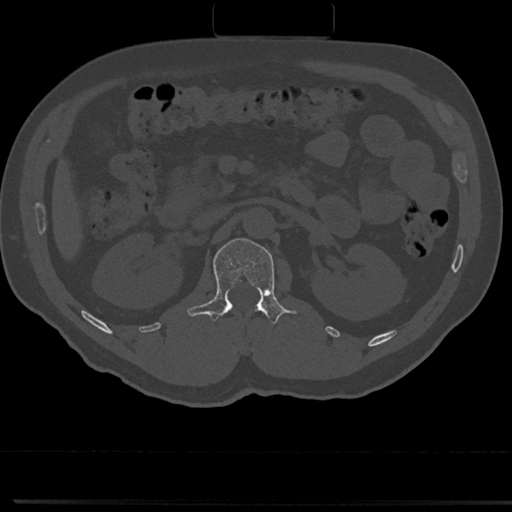
CT including the spine, one axial slice; slice 87 of 817 in the series (ordered by position); reconstruction kernel Br40s/3; 120 kVp; bone window (W 1800 / L 400 HU); 0.5 mm slice thickness; 512 × 512 image matrix. Male patient, age 61 years. Case-level facts recorded for this patient, not image findings: primary cancer: prostate.
Outlined on this slice (semi-automatically segmented with operator editing):
- L1 vertebra: bounding box [x1, y1, x2, y2] px = [191, 239, 287, 325]